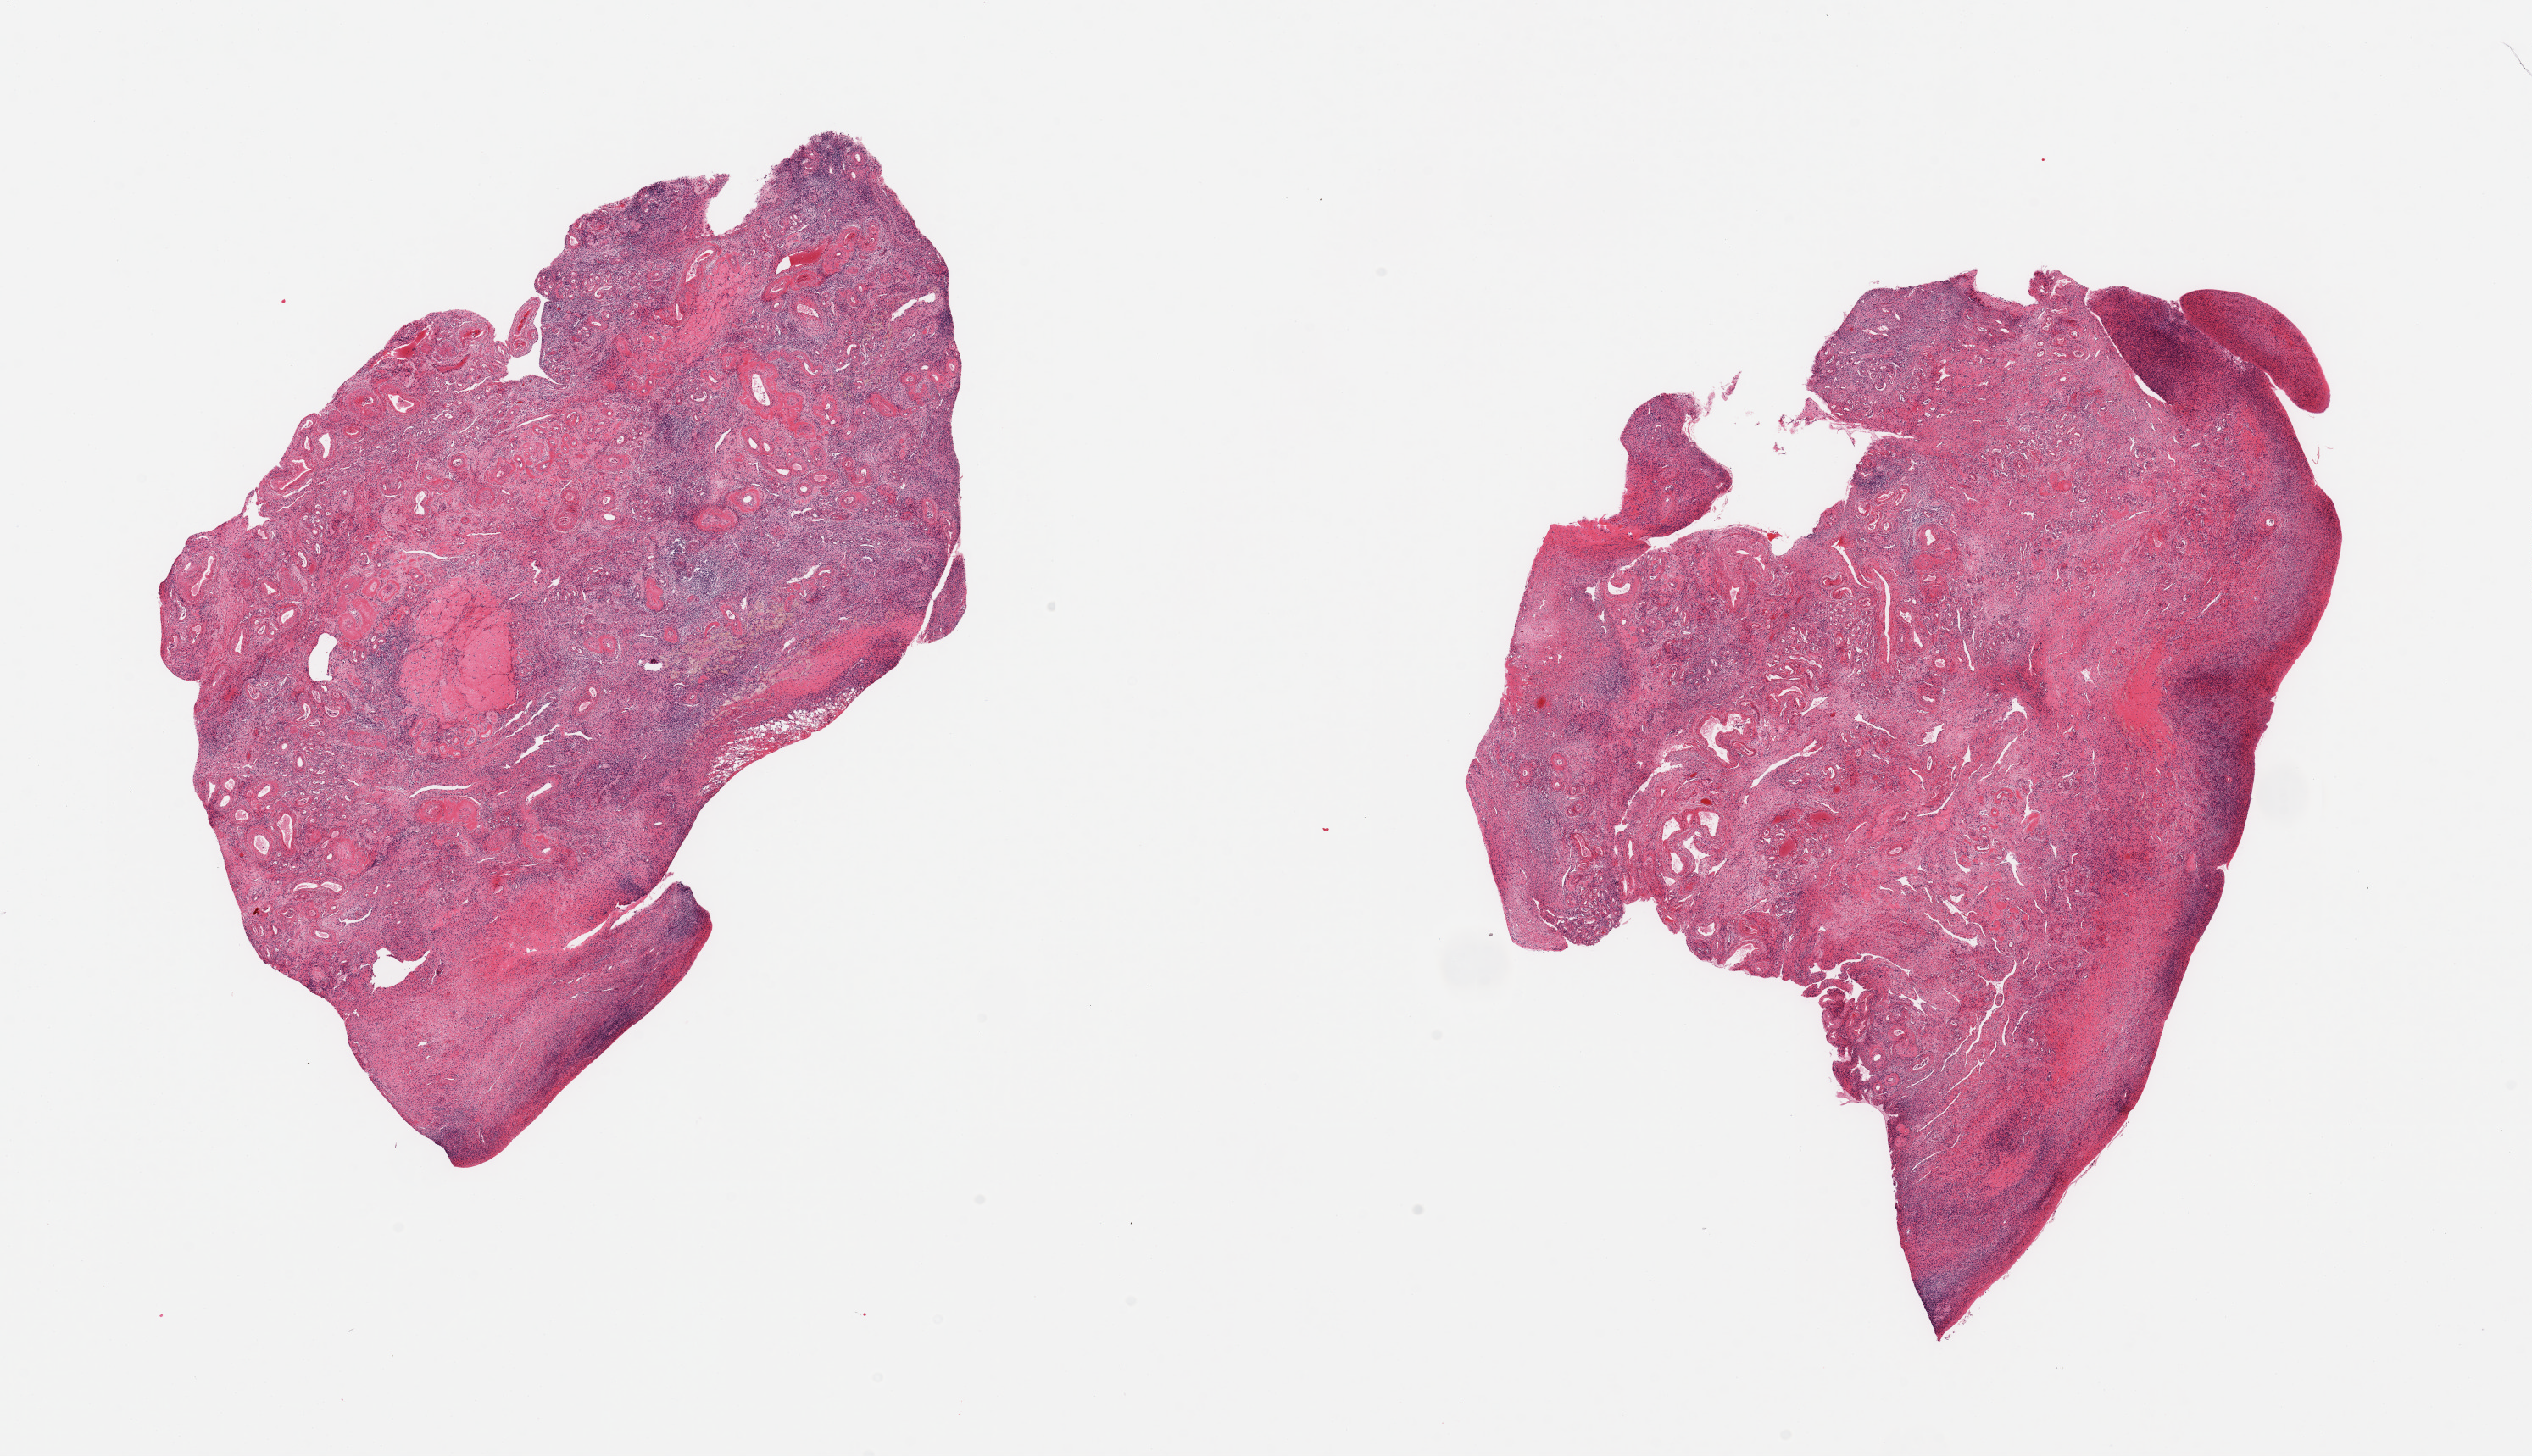
Whole-slide image, hematoxylin and eosin (H&E) stain — a low-resolution overview of the entire scanned area, about 23.6 x 13.6 mm (acquisition: 20x scan), PAXgene-fixed paraffin-embedded (PFPE) section, section of ovary (target tissue), donor tissue sample. Donor: female.
* review note (as recorded): 2 pieces, post menopausal atrophy, no abnormalities